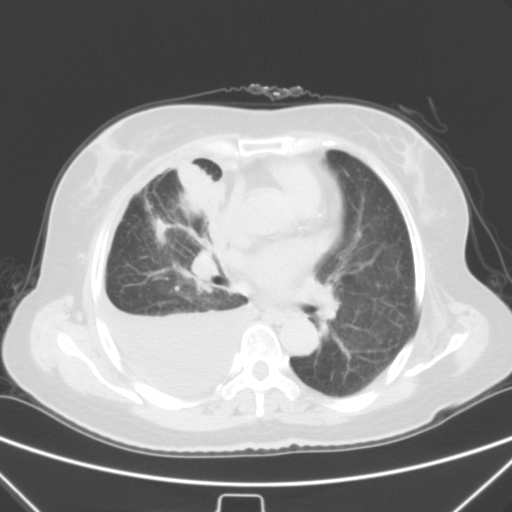
Chest CT, one axial slice; slice 33 of 55 in the series (ordered by position); lung window (W 1500 / L -600 HU); 512 × 512 image matrix. Patient: female, 66 years. From the clinical record (not read from this slice): clinical TNM (as recorded): T2 N0 M1.
Structures marked on this image (bounding box drawn by a radiologist):
- lung tumour (recorded histology: adenocarcinoma): bounding box <173,156,227,229> (left, top, right, bottom; pixels)